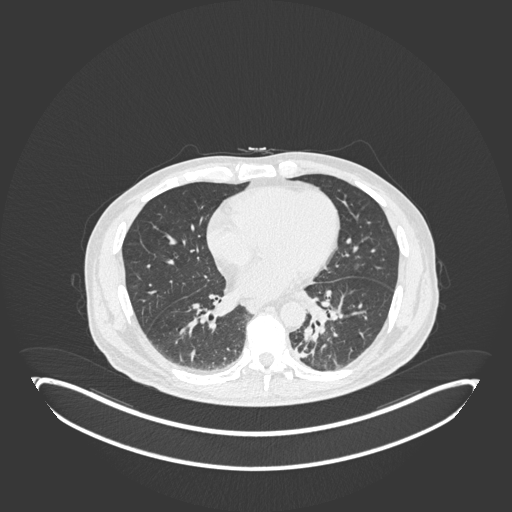
Chest CT, one axial slice. Slice 65 of 251 in the series (ordered by position). Reconstruction kernel B30f. 120 kVp. Lung window (W 1500 / L -600 HU). 1 mm slice thickness. 512 × 512 image matrix, field of view 500 × 500 mm. Male patient, age 72 years. Case-level facts recorded for this patient, not image findings: clinical TNM (as recorded): T2b N0 M1.
Annotated regions visible in this slice (bounding box drawn by a radiologist):
- lung tumour (recorded histology: adenocarcinoma): bounding box <295,323,319,360> (left, top, right, bottom; pixels)